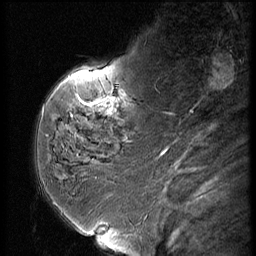
Breast MRI (dynamic contrast-enhanced), one sagittal slice; slice 15 of 56 in the series (ordered by position); dynamic contrast-enhanced series, image 2 of 3 at this slice position (ordered by acquisition); 1.5 T; TE 4.2 ms, TR 9 ms; 2.5 mm slice thickness; 256 × 256 image matrix, field of view 180 × 180 mm. Female patient, age 59 years. From the clinical record (not read from this slice): setting: breast cancer imaged before/during neoadjuvant chemotherapy; receptor status: HER2-positive.
Outlined on this slice (semi-automatically segmented with operator editing):
- analysis volume of interest (the breast-tissue region the enhancement analysis was run in; not a lesion): bounding box [x1, y1, x2, y2] px = [44, 66, 151, 135]
- tumour enhancement mask (voxels above the 140 % enhancement threshold inside the analysis volume of interest): [96, 96, 114, 115]